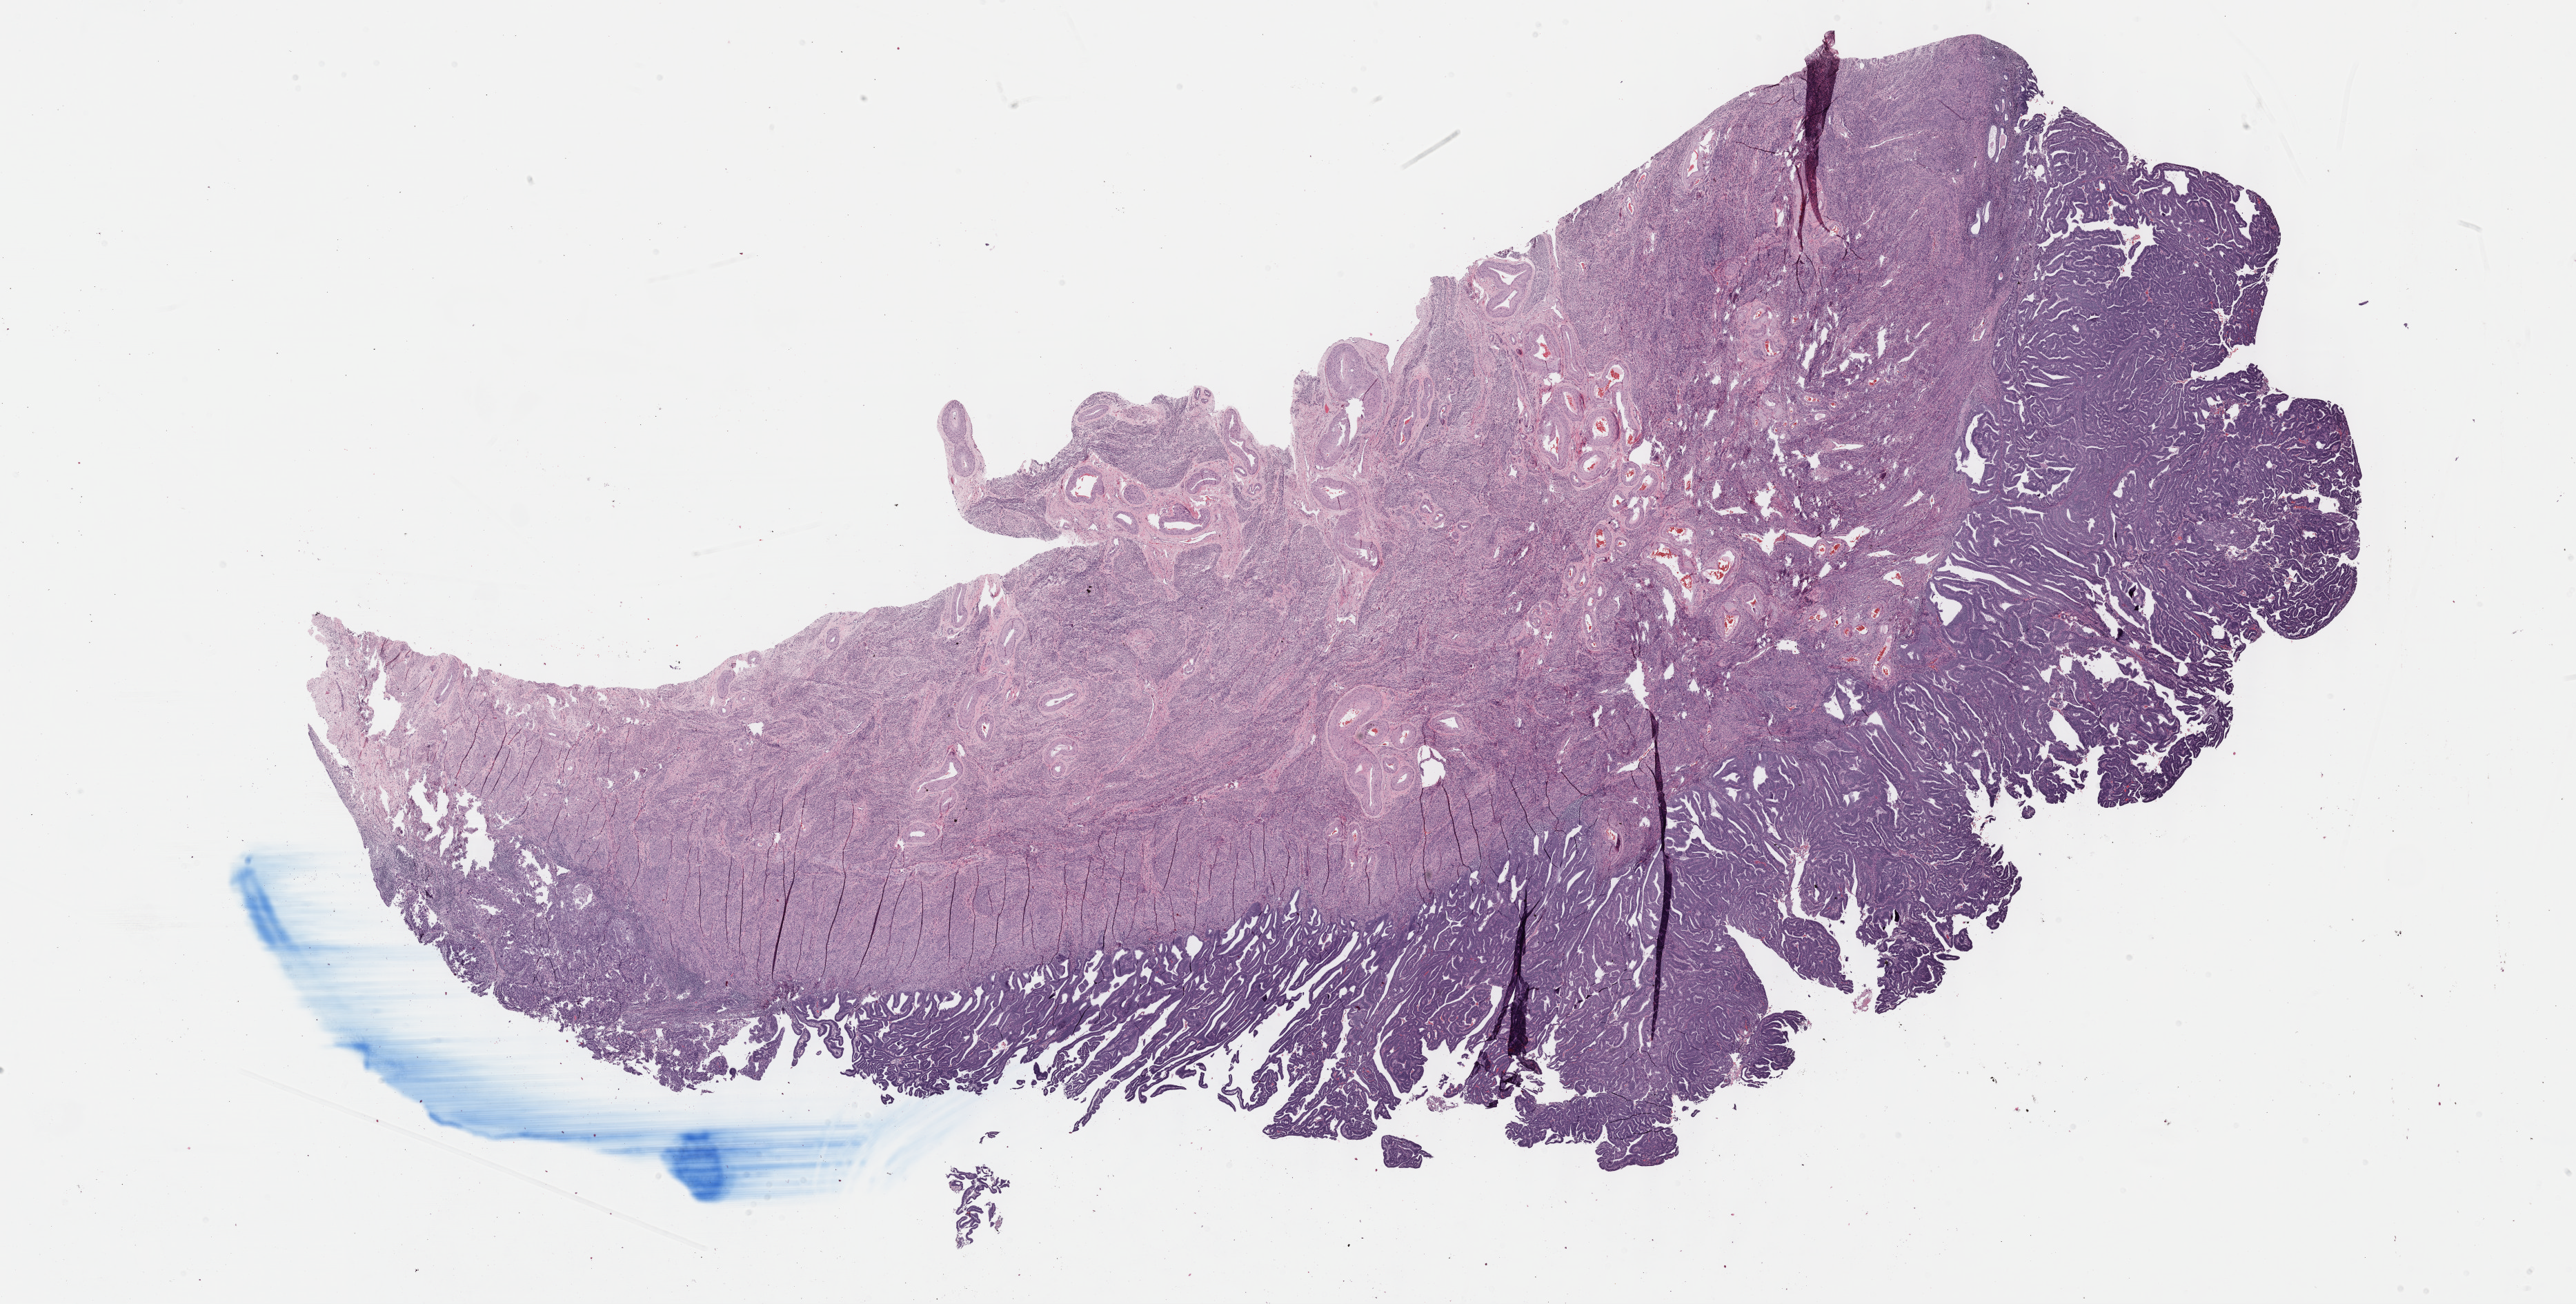
H&E-stained whole-slide image — a low-resolution overview of the entire scanned area, about 30.2 x 15.3 mm (slide scanned at 40x), formalin-fixed paraffin-embedded (FFPE) diagnostic section, uterus, primary tumour sample. Patient: female, age at initial diagnosis 57 years. Histologic grade: G2 (moderately differentiated).
• pathologic diagnosis: Endometrioid adenocarcinoma, NOS (endometrium)
• FIGO stage: II